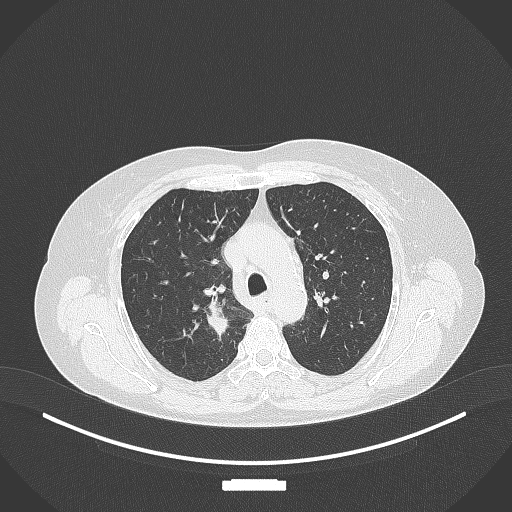
Chest CT, one axial slice; slice 271 of 357 in the series (ordered by position); lung window (W 1500 / L -600 HU); 1 mm slice thickness; 512 × 512 image matrix. Patient: female, 62 years. From the clinical record (not read from this slice): clinical TNM (as recorded): T1c N1 M0.
Annotated regions visible in this slice (bounding box drawn by a radiologist):
- lung tumour (recorded histology: squamous cell carcinoma): box from (x=205, y=301) to (x=231, y=344) px